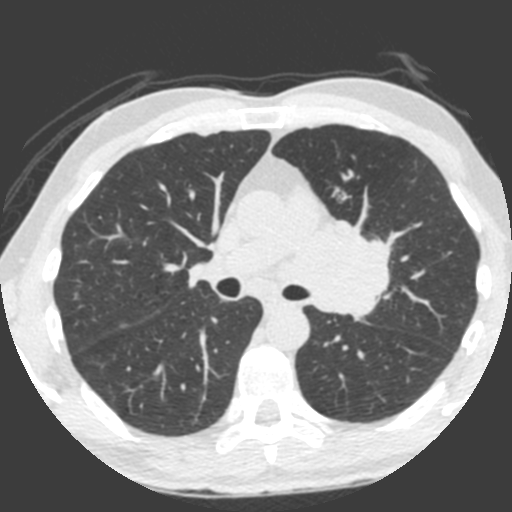
Low-dose screening chest CT, one axial slice. Slice 134 of 212 in the series (ordered by position). 120 kVp. Lung window (W 1500 / L -600 HU). 2 mm slice thickness. 512 × 512 image matrix, field of view 315 × 315 mm.
Outlined on this slice (expert manual segmentation):
- lesion 1 (tumor, upper lobe of left lung): bounding box (x1, y1, x2, y2) in pixels: (317, 222, 392, 318)